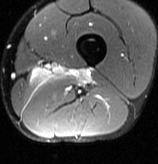
MRI of an extremity soft-tissue mass, one axial slice. Slice 18 of 70 in the series (ordered by position). T2-weighted fat-saturated. MR volume resampled by the dataset authors to the PET/CT grid (not the native acquisition matrix). 3.27 mm slice thickness. 158 × 164 image matrix. Male patient. Case-level facts recorded for this patient, not image findings: histological type: extraskeletal osteosarcoma; grade: high; site of the primary tumour: left adductur.
Structures marked on this image (expert contour drawn on MRI and transferred to this co-registered scan by the dataset authors):
- gross tumour volume (mass): bounding box (x1, y1, x2, y2) in pixels: (49, 66, 91, 84)